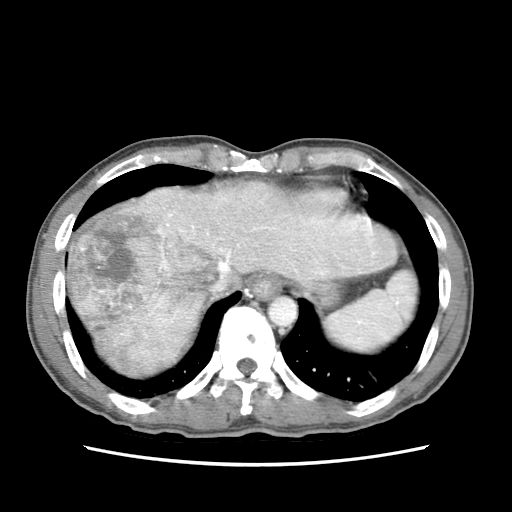
Contrast-enhanced abdominal CT (liver protocol), one axial slice. Position 63 of 79 along the scan axis. Soft-tissue window (W 400 / L 40 HU). 512 × 512 image matrix, field of view 320 × 320 mm. From the clinical record (not read from this slice): diagnosis: hepatocellular carcinoma (patient treated with transarterial chemoembolisation; whether this scan precedes or follows treatment is not stated here); TNM stage (as recorded): Stage-IIIB; Child-Pugh class: A; tumour differentiation: moderately differentiated; tumour nodularity: multinodular.
Structures marked on this image (semi-automatically segmented with operator editing):
- abdominal aorta: bounding box [x1, y1, x2, y2] px = [269, 298, 296, 326]
- liver parenchyma outside the tumour (the mass and vessels are separate outlines, so this box may not span the whole liver): [66, 180, 400, 372]
- mass: [67, 189, 218, 375]
- liver vessels: [165, 191, 344, 269]